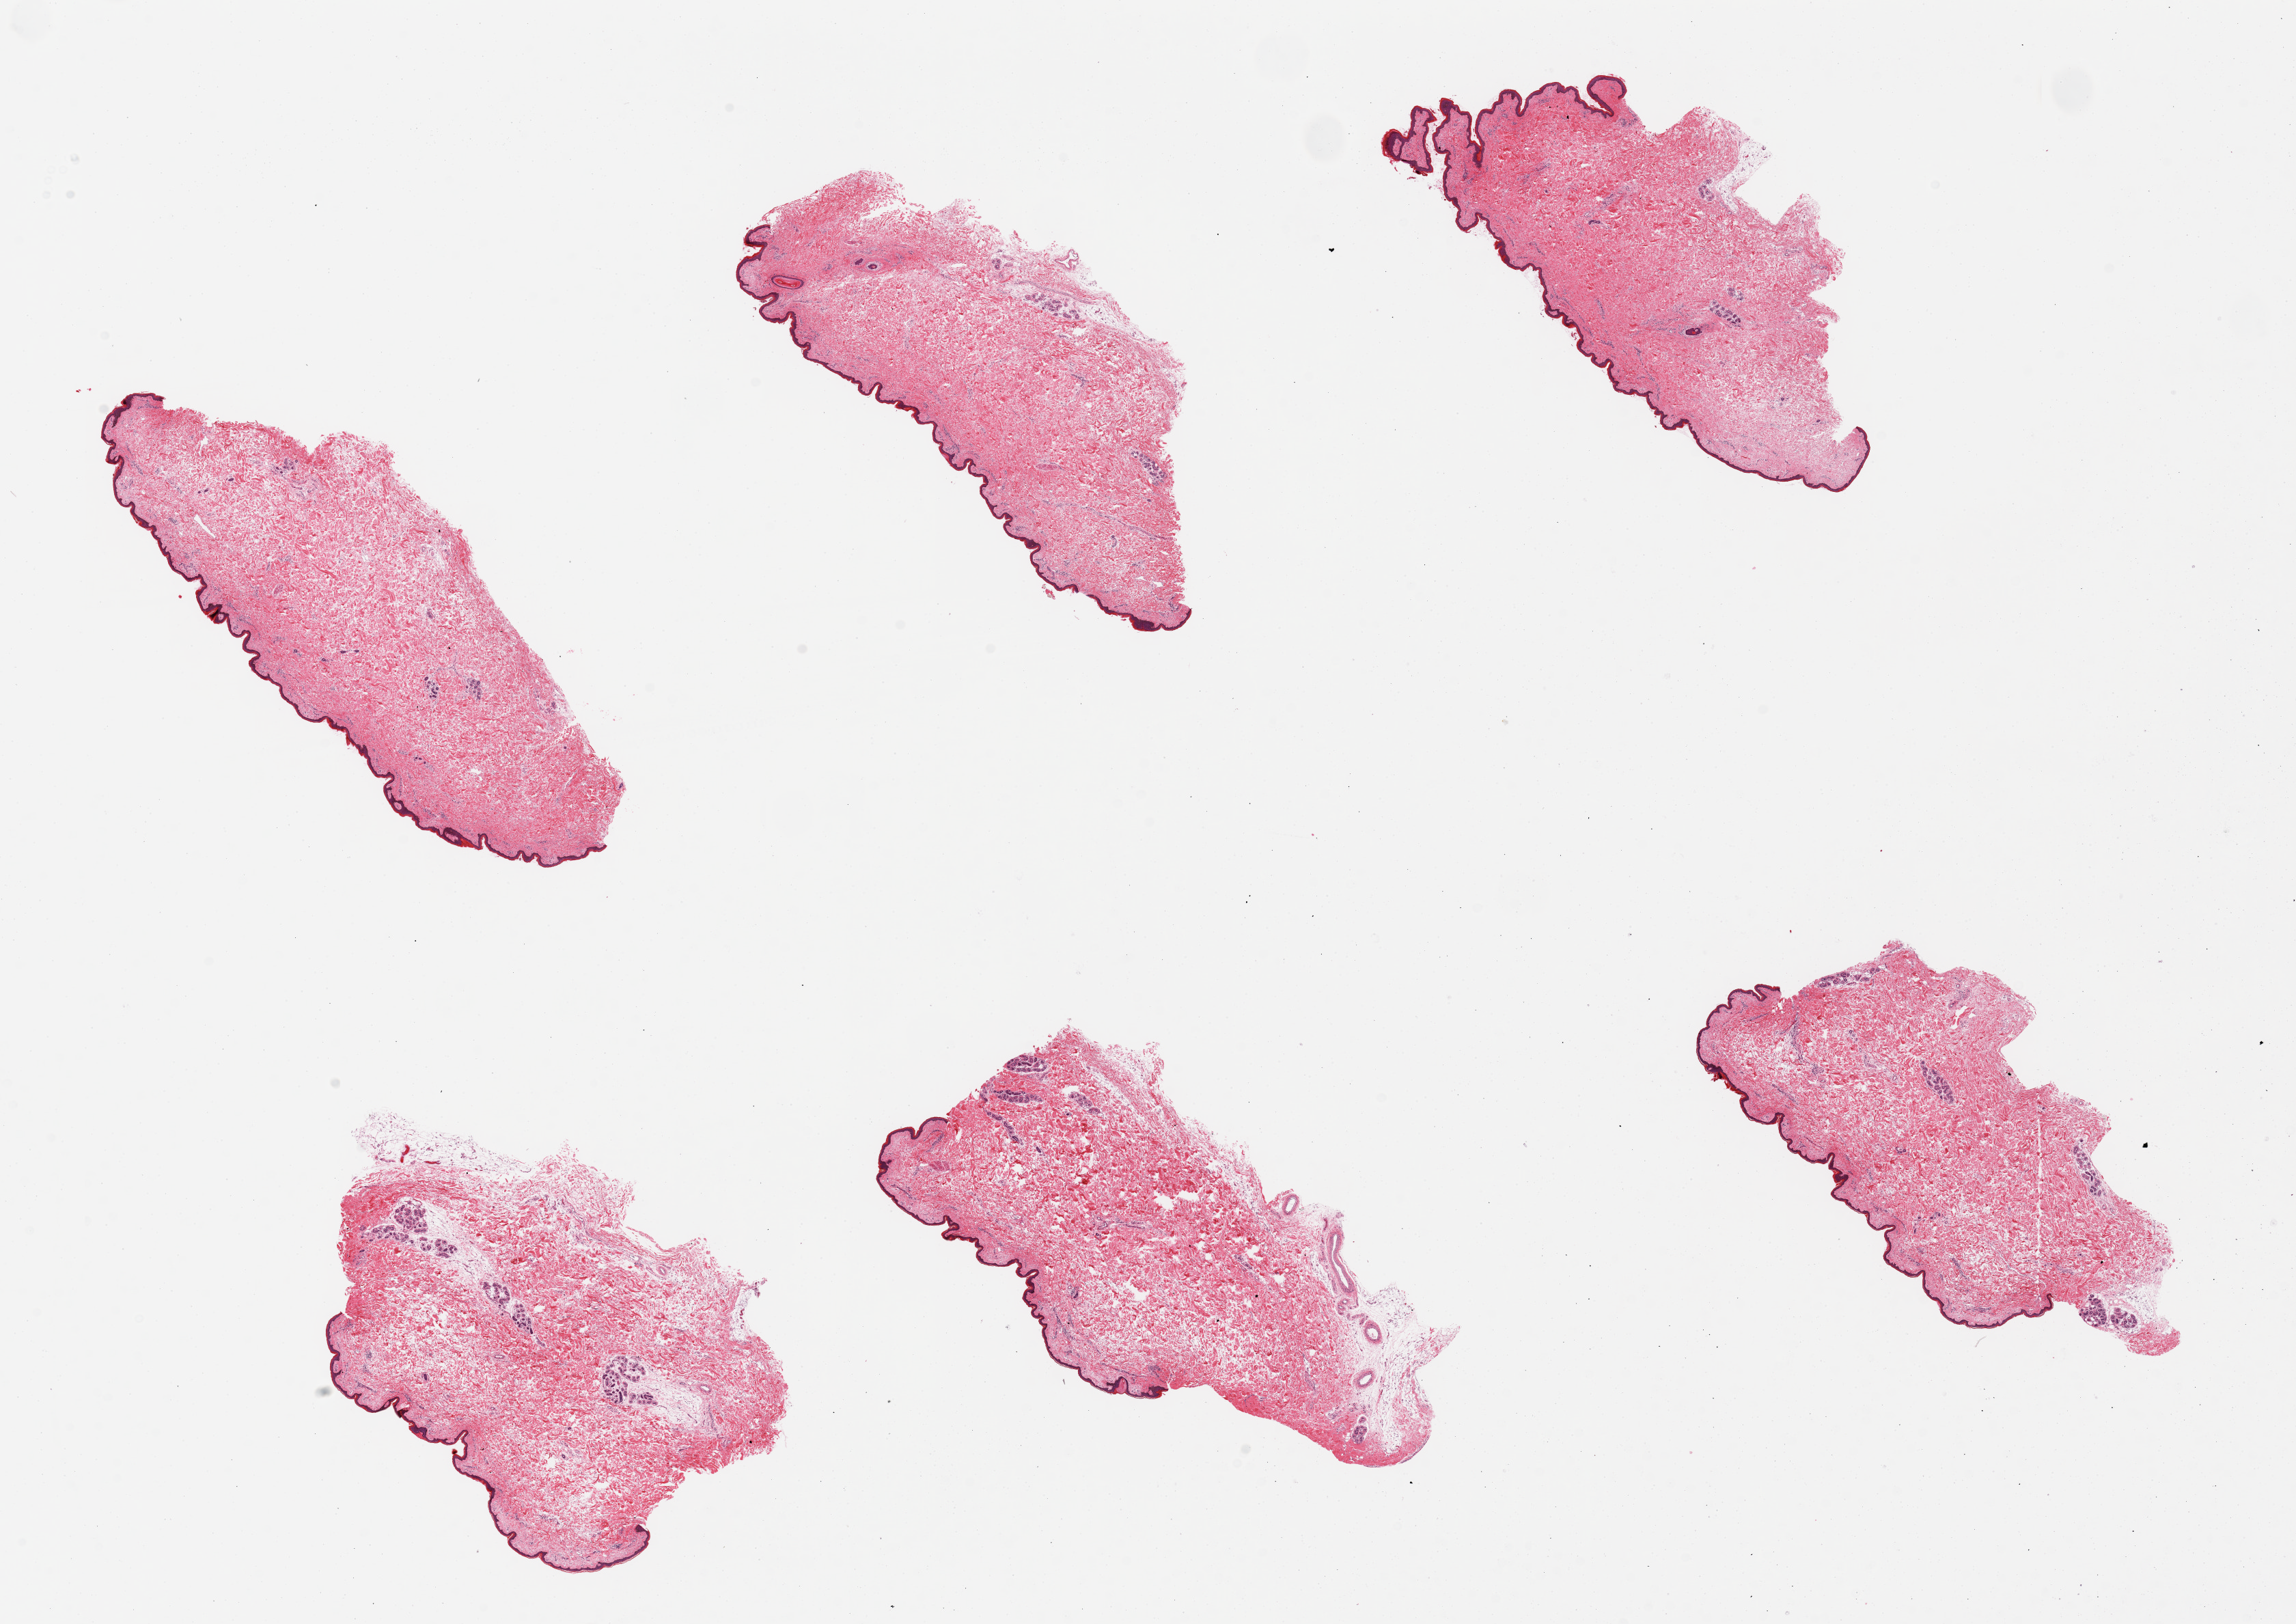
Digitized haematoxylin and eosin-stained section — a low-resolution overview of the entire scanned area, about 26.6 x 18.8 mm (acquisition: 20x scan), PAXgene-fixed, paraffin-embedded tissue, target tissue: skin of suprapubic region, donor tissue sample. Donor: female.
Review note (as recorded): 6 pieces, minimal fat, squamous epithelium is ~50 microns, ~3% thickness.